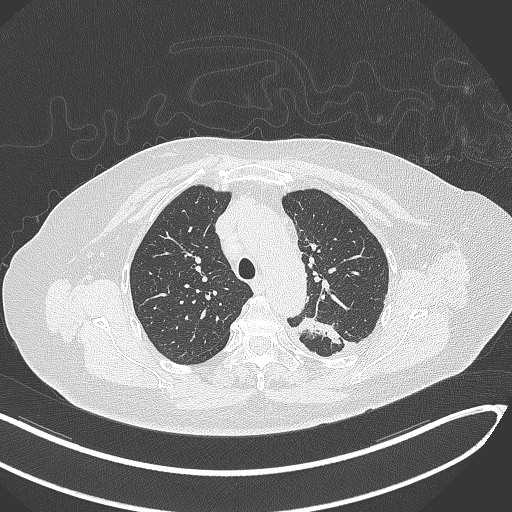
Chest CT, one axial slice. Lung window (W 1500 / L -600 HU). 512 × 512 image matrix, field of view 400 × 400 mm. Female patient, age 76 years. Case-level facts recorded for this patient, not image findings: clinical TNM (as recorded): T1c N0 M0.
Outlined on this slice (bounding box drawn by a radiologist):
- lung tumour (recorded histology: adenocarcinoma): bounding box [x1, y1, x2, y2] px = [293, 312, 342, 348]